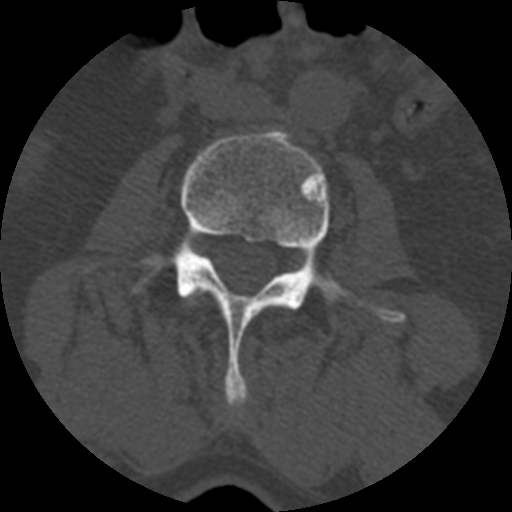
CT including the spine, one axial slice; slice 307 of 399 in the series (ordered by position); reconstruction kernel STANDARD; bone window (W 1800 / L 400 HU); 512 × 512 image matrix. Patient age 71 years. Case-level facts recorded for this patient, not image findings: primary cancer: prostate.
Structures marked on this image (semi-automatically segmented with operator editing):
- L2 vertebra: bounding box [x1, y1, x2, y2] px = [188, 292, 200, 302]
- L3 vertebra: [82, 131, 406, 408]